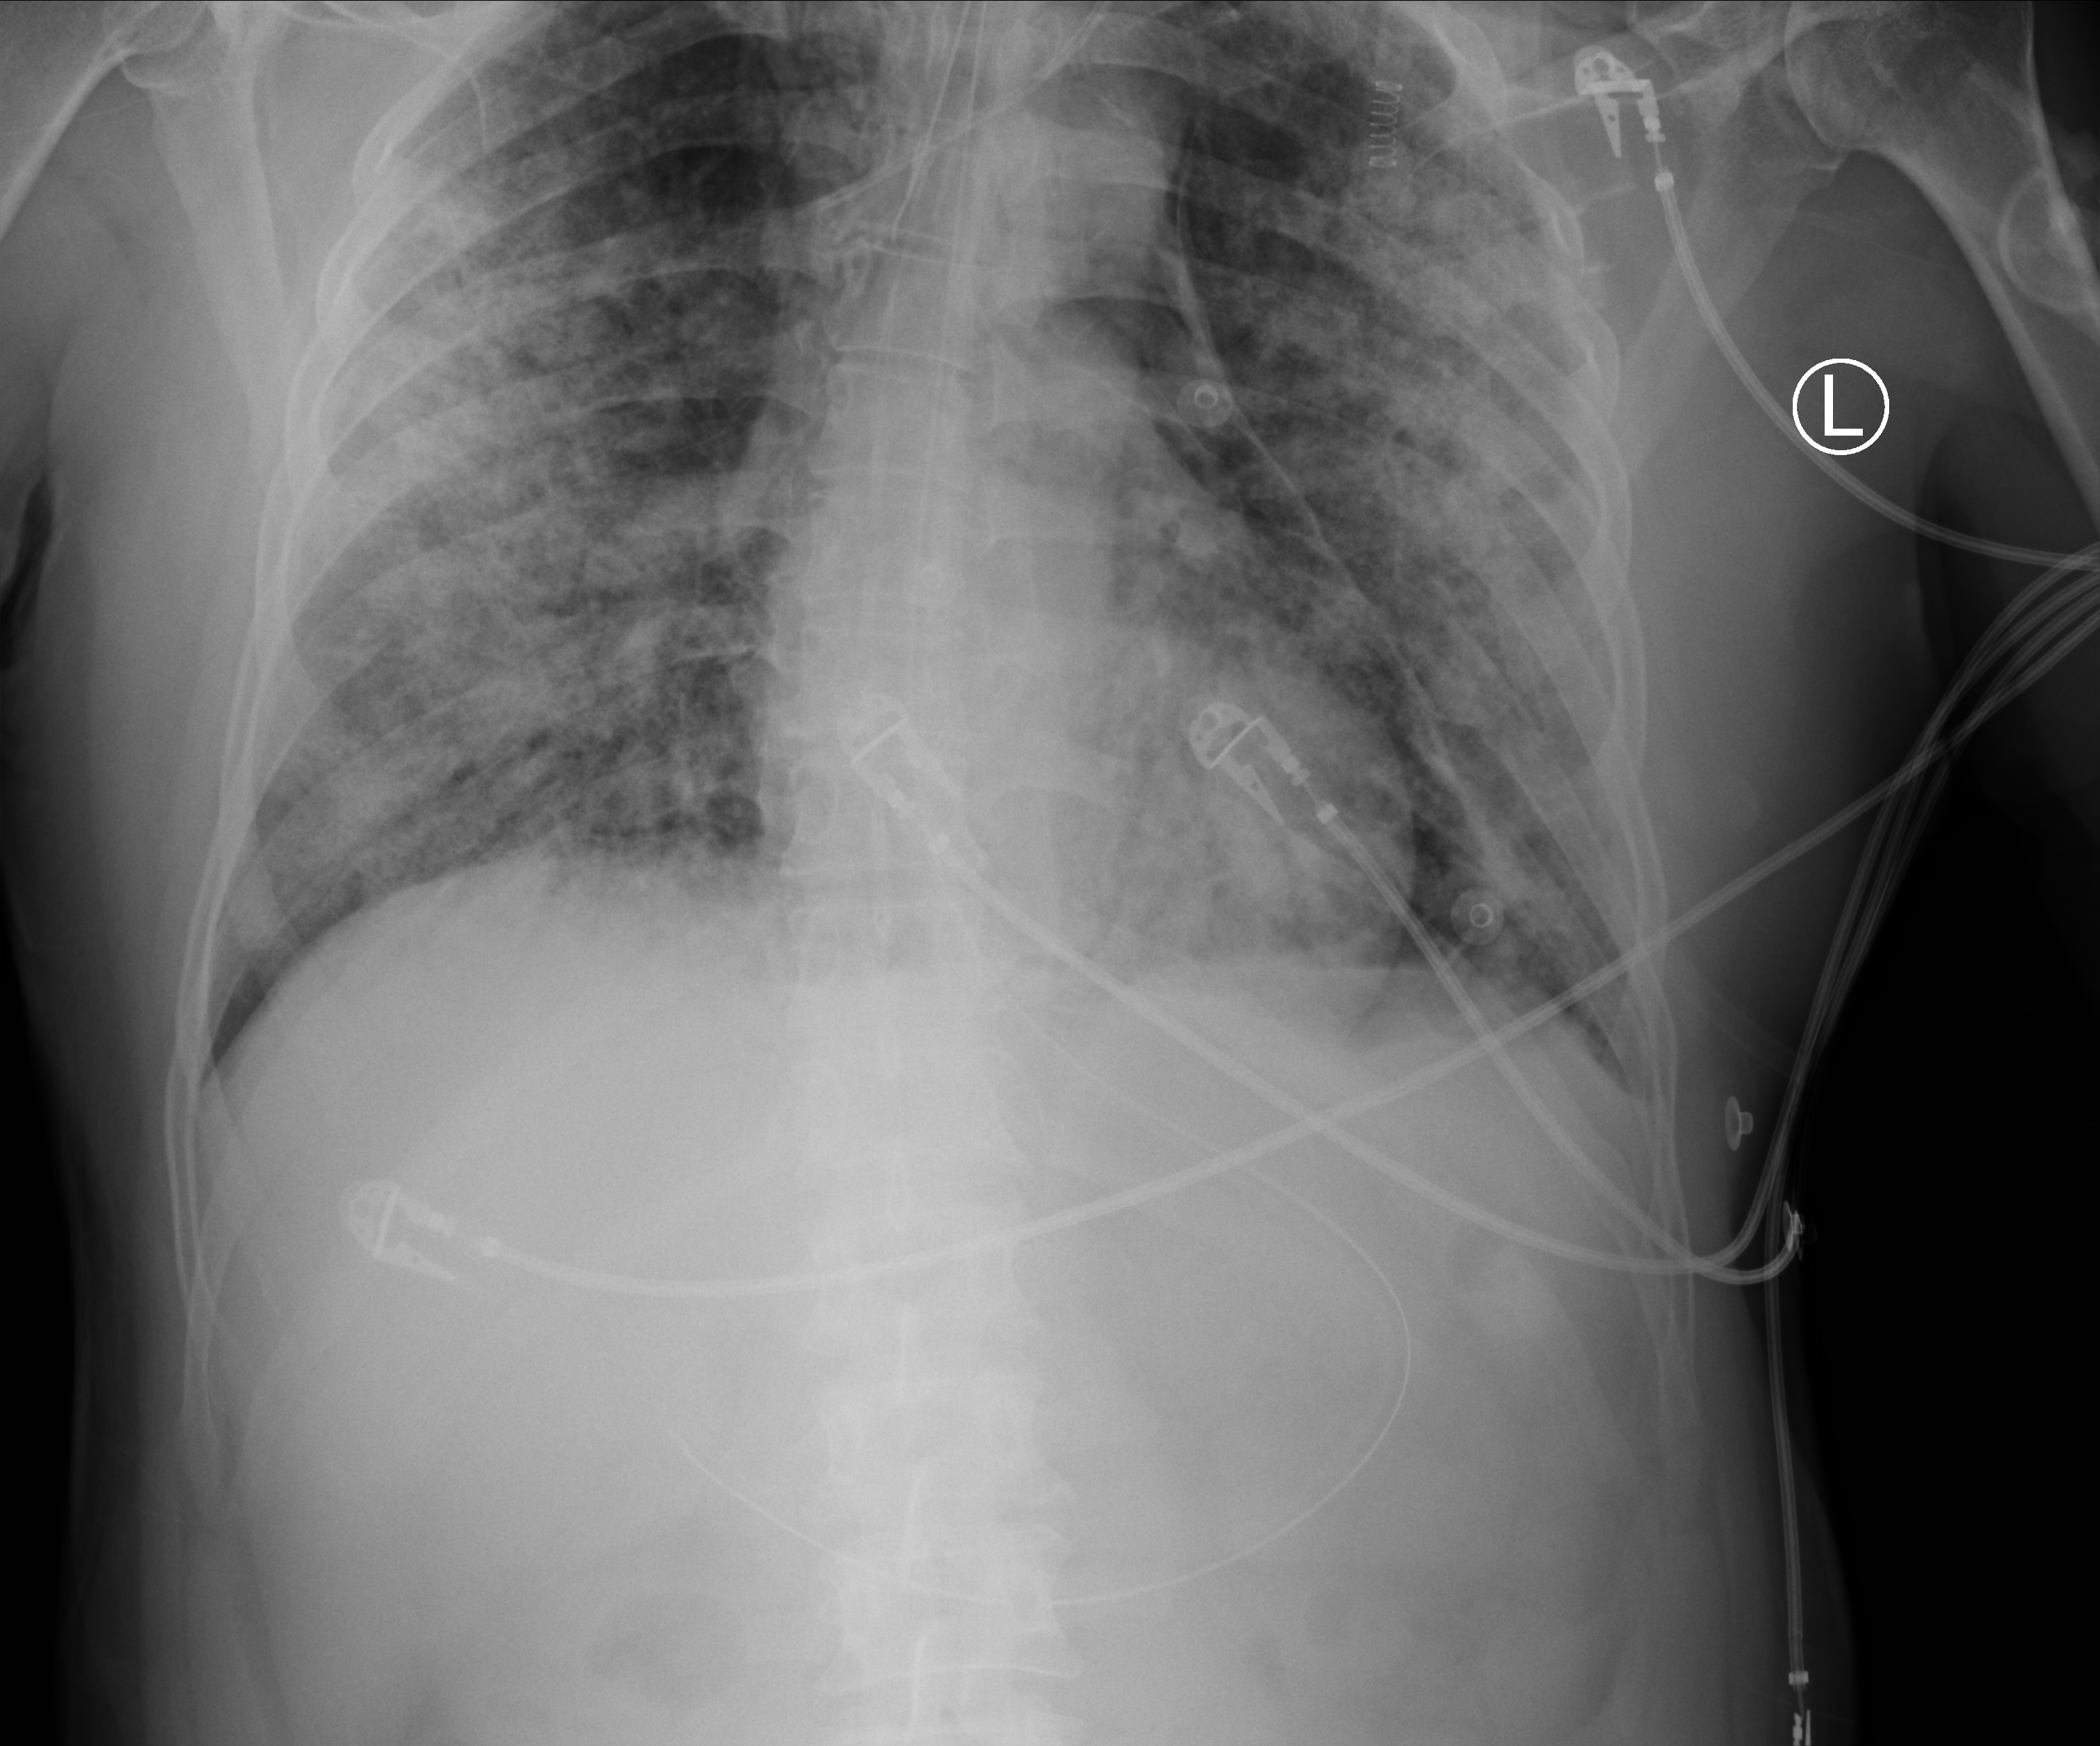
Bedside chest radiograph (computed radiography), anteroposterior (AP) projection. Male patient hospitalised with COVID-19, age 60–74 years.
Admission-level facts for this patient (not findings on this image; timing relative to this image not recorded): COPD (admission record): no; length of hospital stay: 65 days.